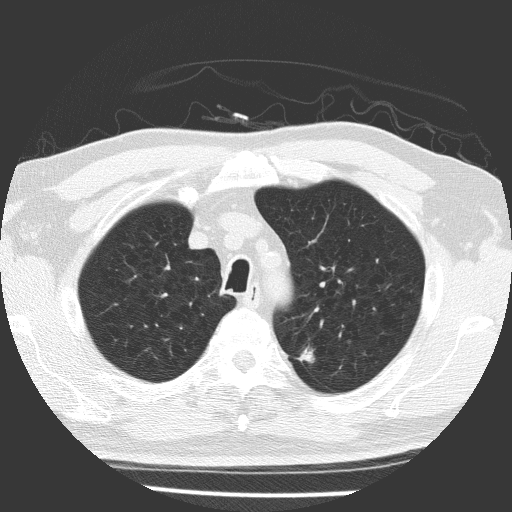
Chest CT (low-dose screening protocol), one axial image, first (baseline) screen, lung window (W 1500 / L -600 HU), 2 mm slice thickness, 120 kVp, slice 36 of 169 in the series. Male, age 64 years at enrolment. Former smoker at enrolment.
- Lesion marked by an expert reader, bounding box [x1, y1, x2, y2] px = [286, 339, 325, 376].
- Reader record for this screening exam (exam-level; its link to the box is not recorded): non-calcified nodule or mass ≥4 mm, left upper lobe, 9 × 7 mm, spiculated (stellate) margins, soft tissue attenuation.
- Official screen result: positive, change unspecified: nodule(s) >= 4 mm or enlarging nodule(s), mass(es), or other non-specific abnormalities suspicious for lung cancer.
- Participant outcome: lung cancer diagnosed 70 days after this screen — adenocarcinoma, NOS, left upper lobe, poorly differentiated (G3), stage IIA (AJCC 6th edition), 9 mm at pathology.